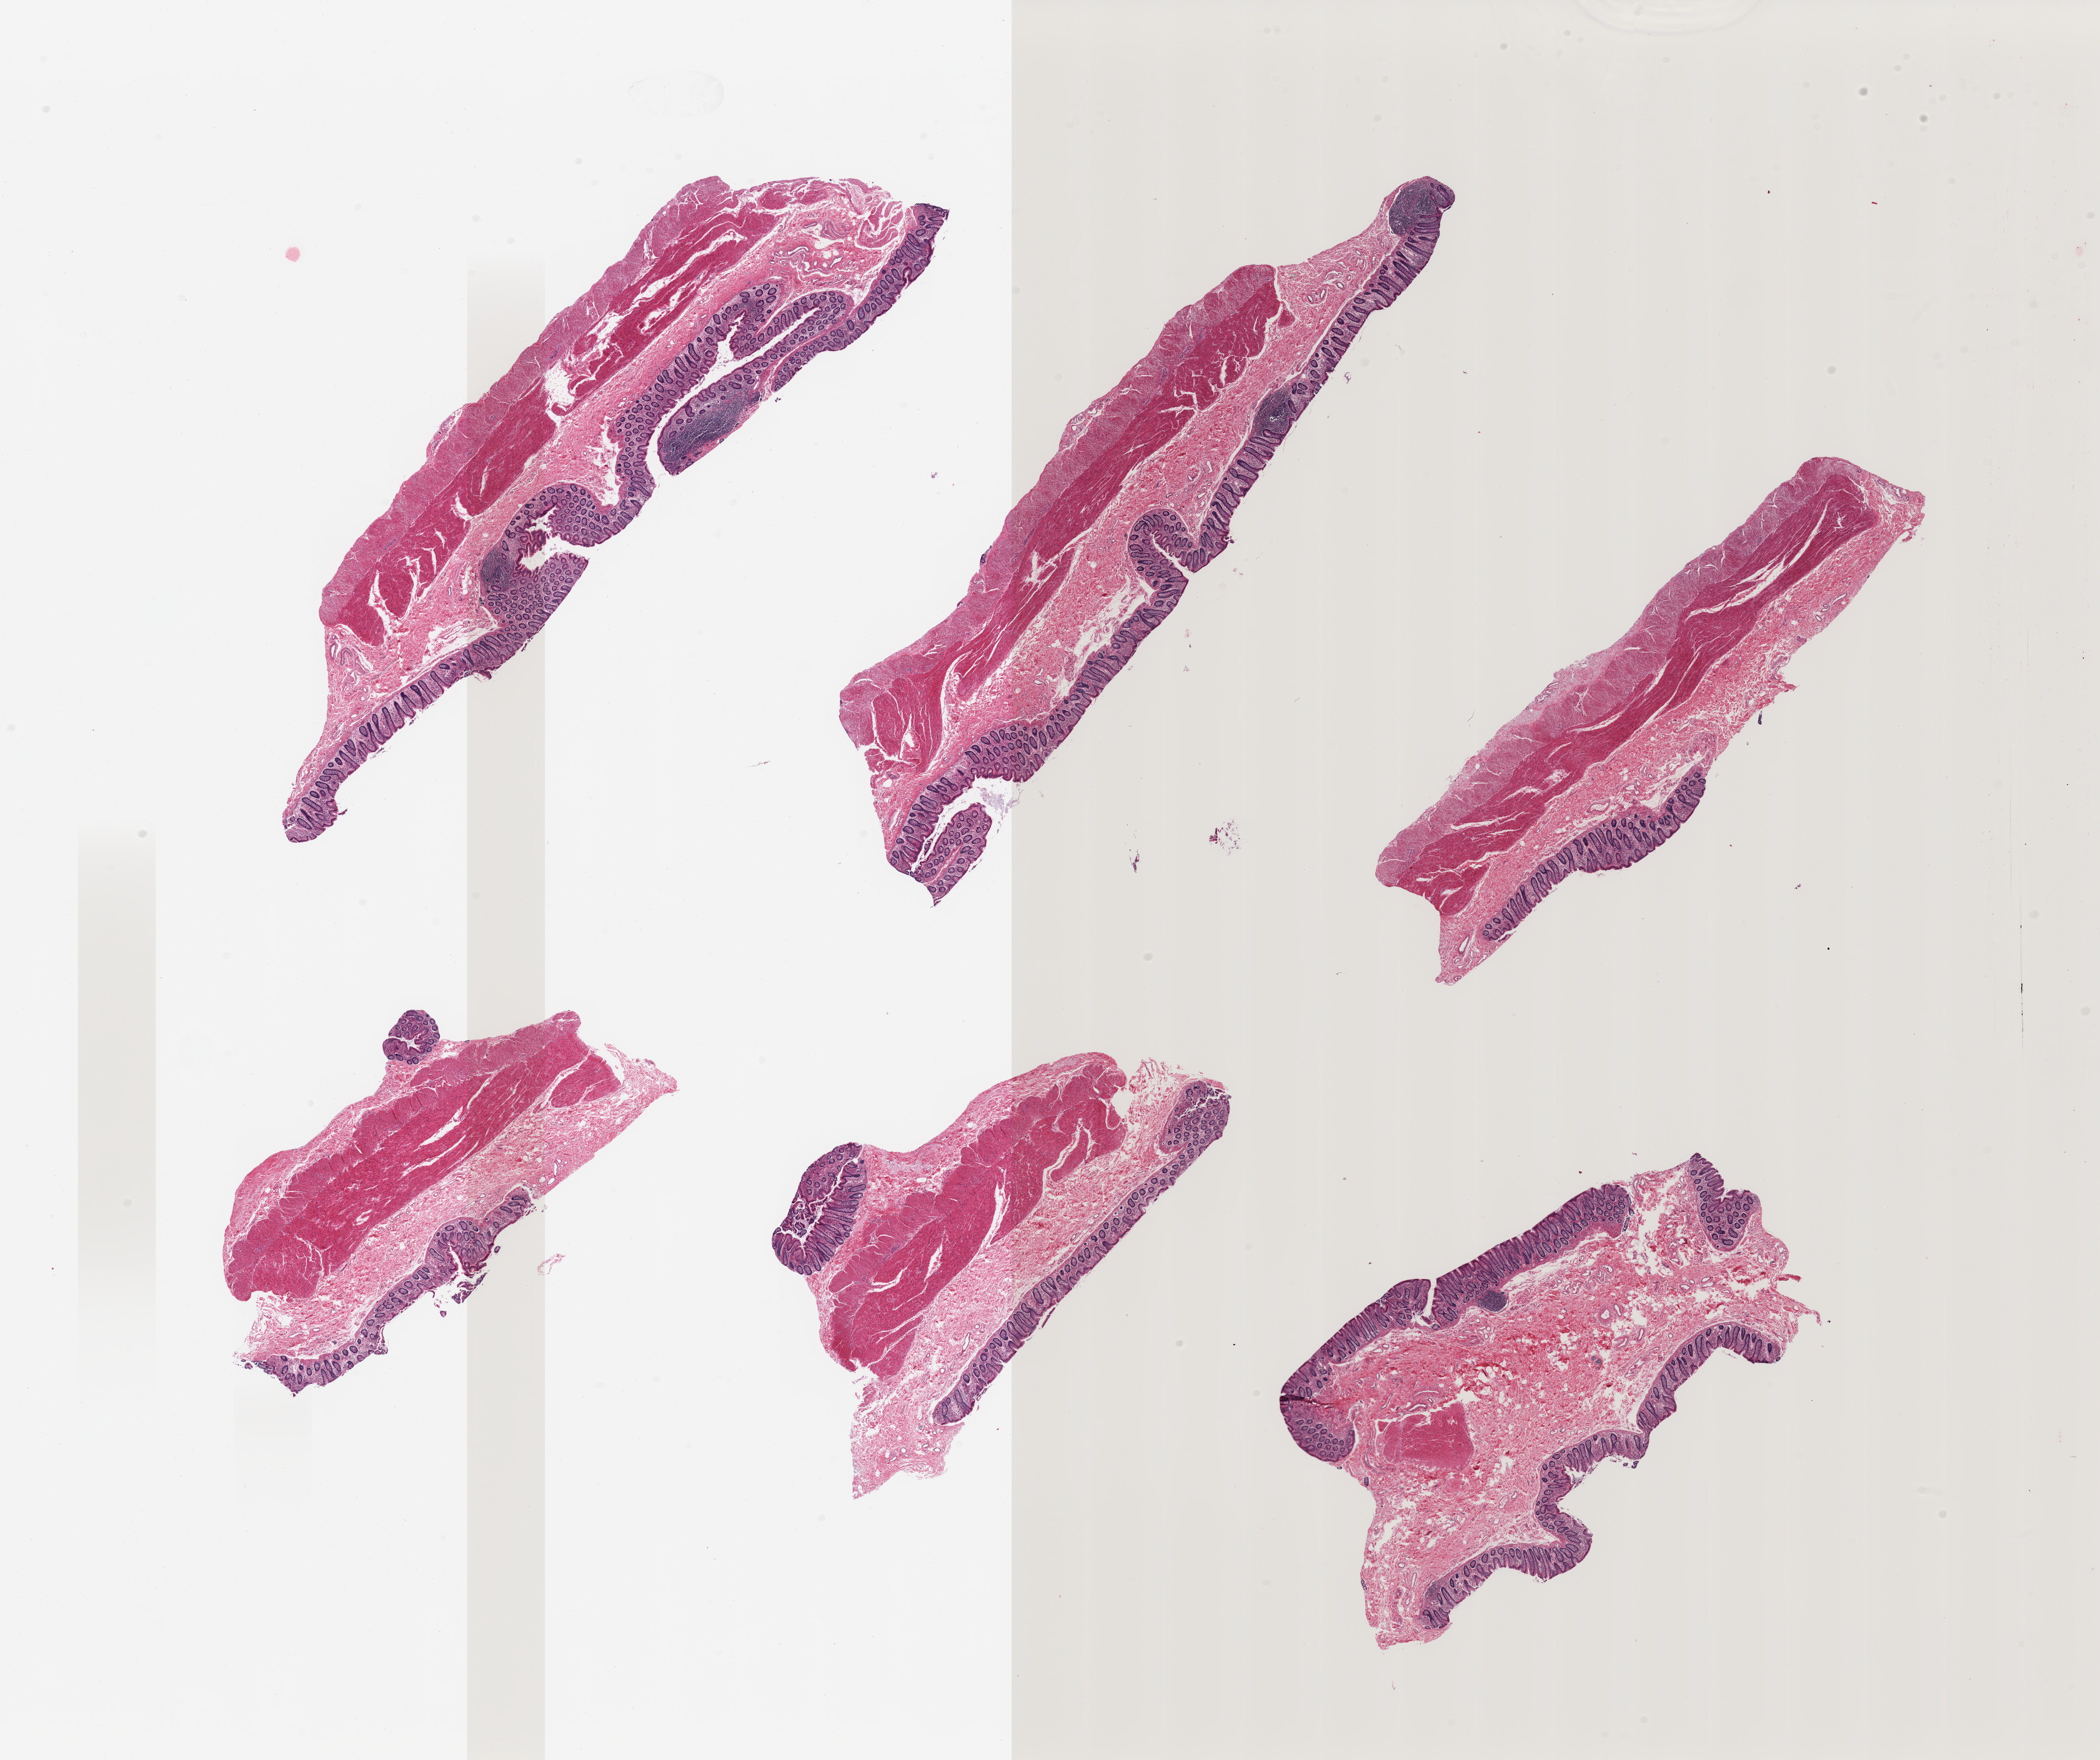
Whole-slide image, H&E stain, brightfield, whole scanned area (about 26.6 x 22.3 mm, acquisition: 20x scan) shown as a low-resolution overview; PAXgene-fixed, paraffin-embedded tissue; sampled site (target tissue): transverse colon; donor tissue sample. Male donor.
* reviewer comment on this tissue sample: 6 pieces; mildly autolyzed mucosa and preserved muscularis